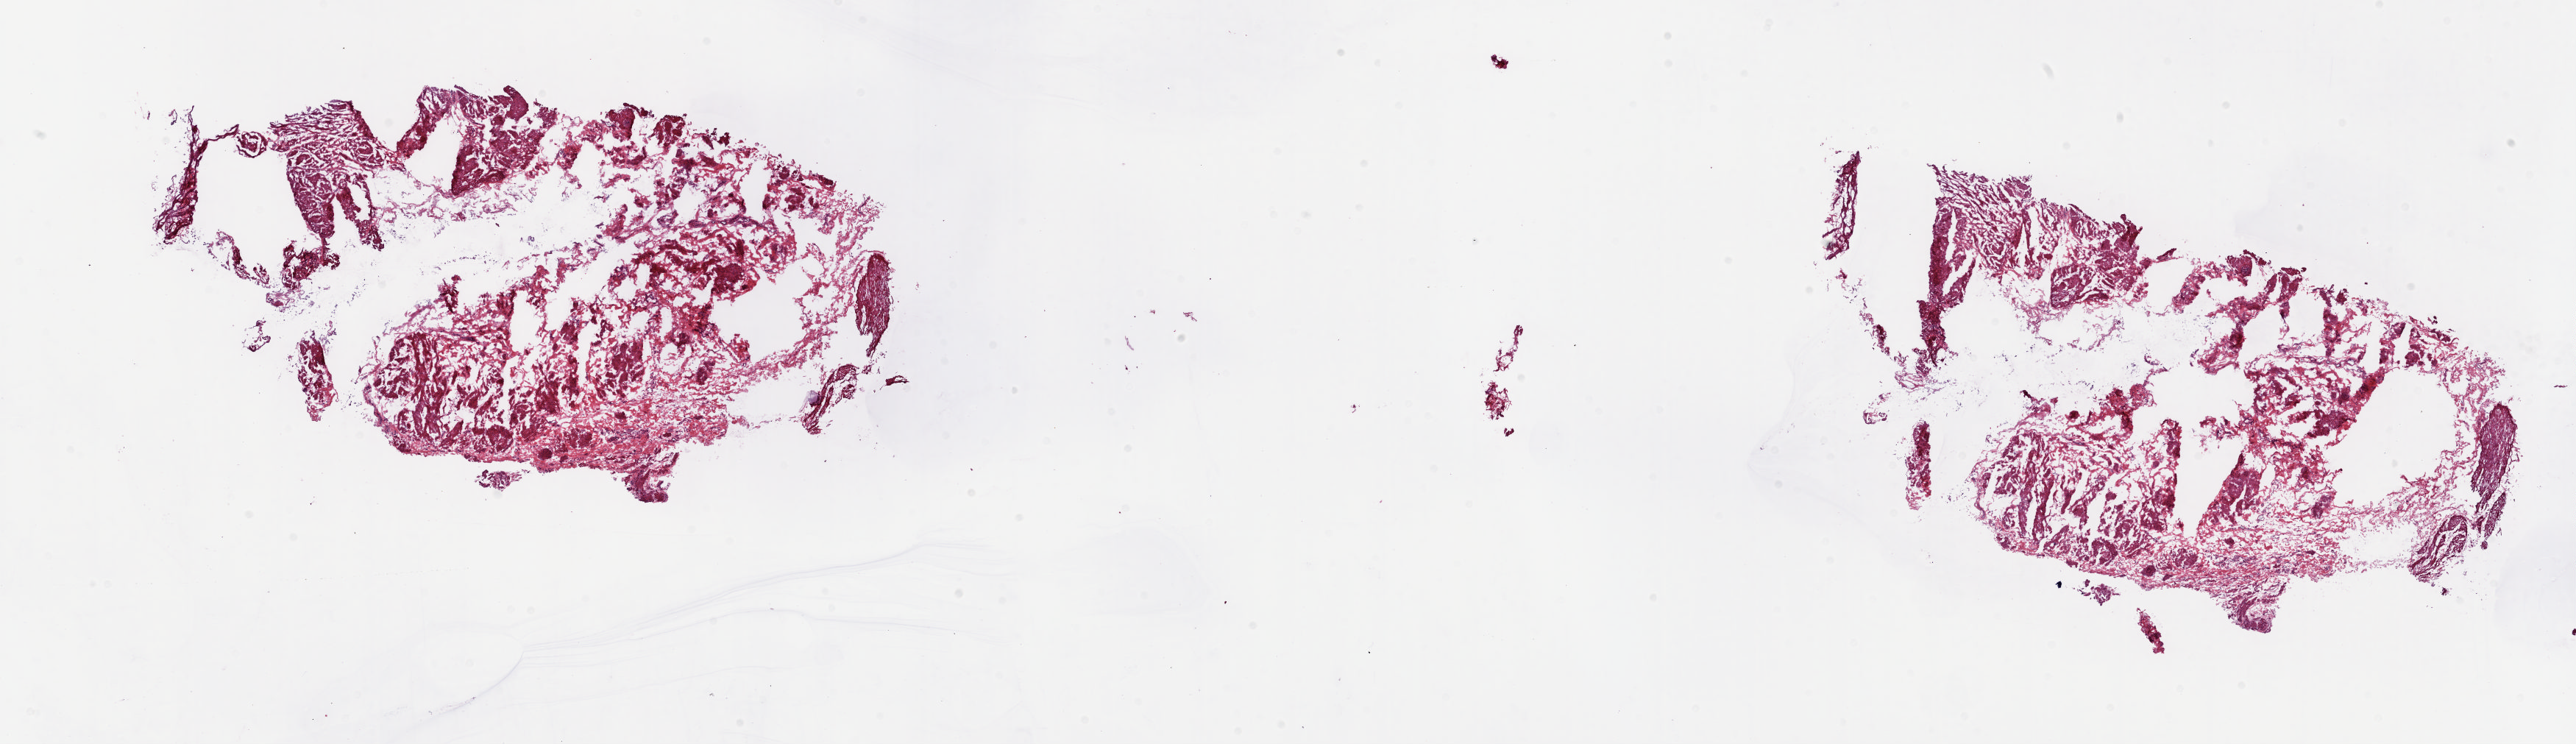
Digitized Hematoxylin and eosin (H&E) stained tissue section (whole slide), low-resolution overview of the scanned area, about 27.8 x 8.0 mm. Frozen section from the top of the tissue portion. Solid tissue normal (non-tumour tissue) sample from the bladder. Male, age 63 years at initial diagnosis. Slide review estimates, as recorded: tumour cells 0%, tumour nuclei 0%, normal cells 100%, stromal cells 0%, necrosis 0%. Inflammatory infiltration, as recorded: lymphocyte infiltration 1%, monocyte infiltration 0%, neutrophil infiltration 0%.
- this section: solid tissue normal (non-tumour) sample from the same patient
- patient diagnosis: Transitional cell carcinoma